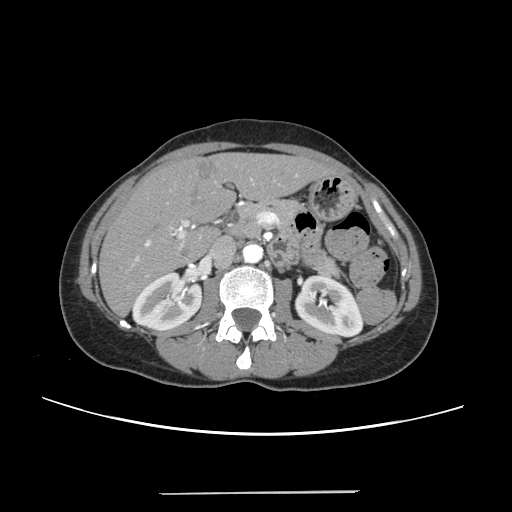
Contrast-enhanced abdominal CT, one axial slice. Position 119 of 240 along the scan axis. Soft-tissue window (W 400 / L 40 HU). 1.25 mm slice thickness. 512 × 512 image matrix, field of view 371 × 371 mm. Female patient, age 60 years. From the clinical record (not read from this slice): diagnosis: colorectal cancer liver metastases, imaged before liver resection; multiple liver metastases: no; largest metastasis: 1.5 cm.
Structures marked on this image (manually delineated by an expert):
- liver: bounding box <101,153,329,314> (left, top, right, bottom; pixels)
- planned liver remnant (the part of the liver to remain after resection): <101,154,329,313>
- portal vein (with intrahepatic branches): <135,179,254,276>
- liver metastasis: <195,161,217,181>